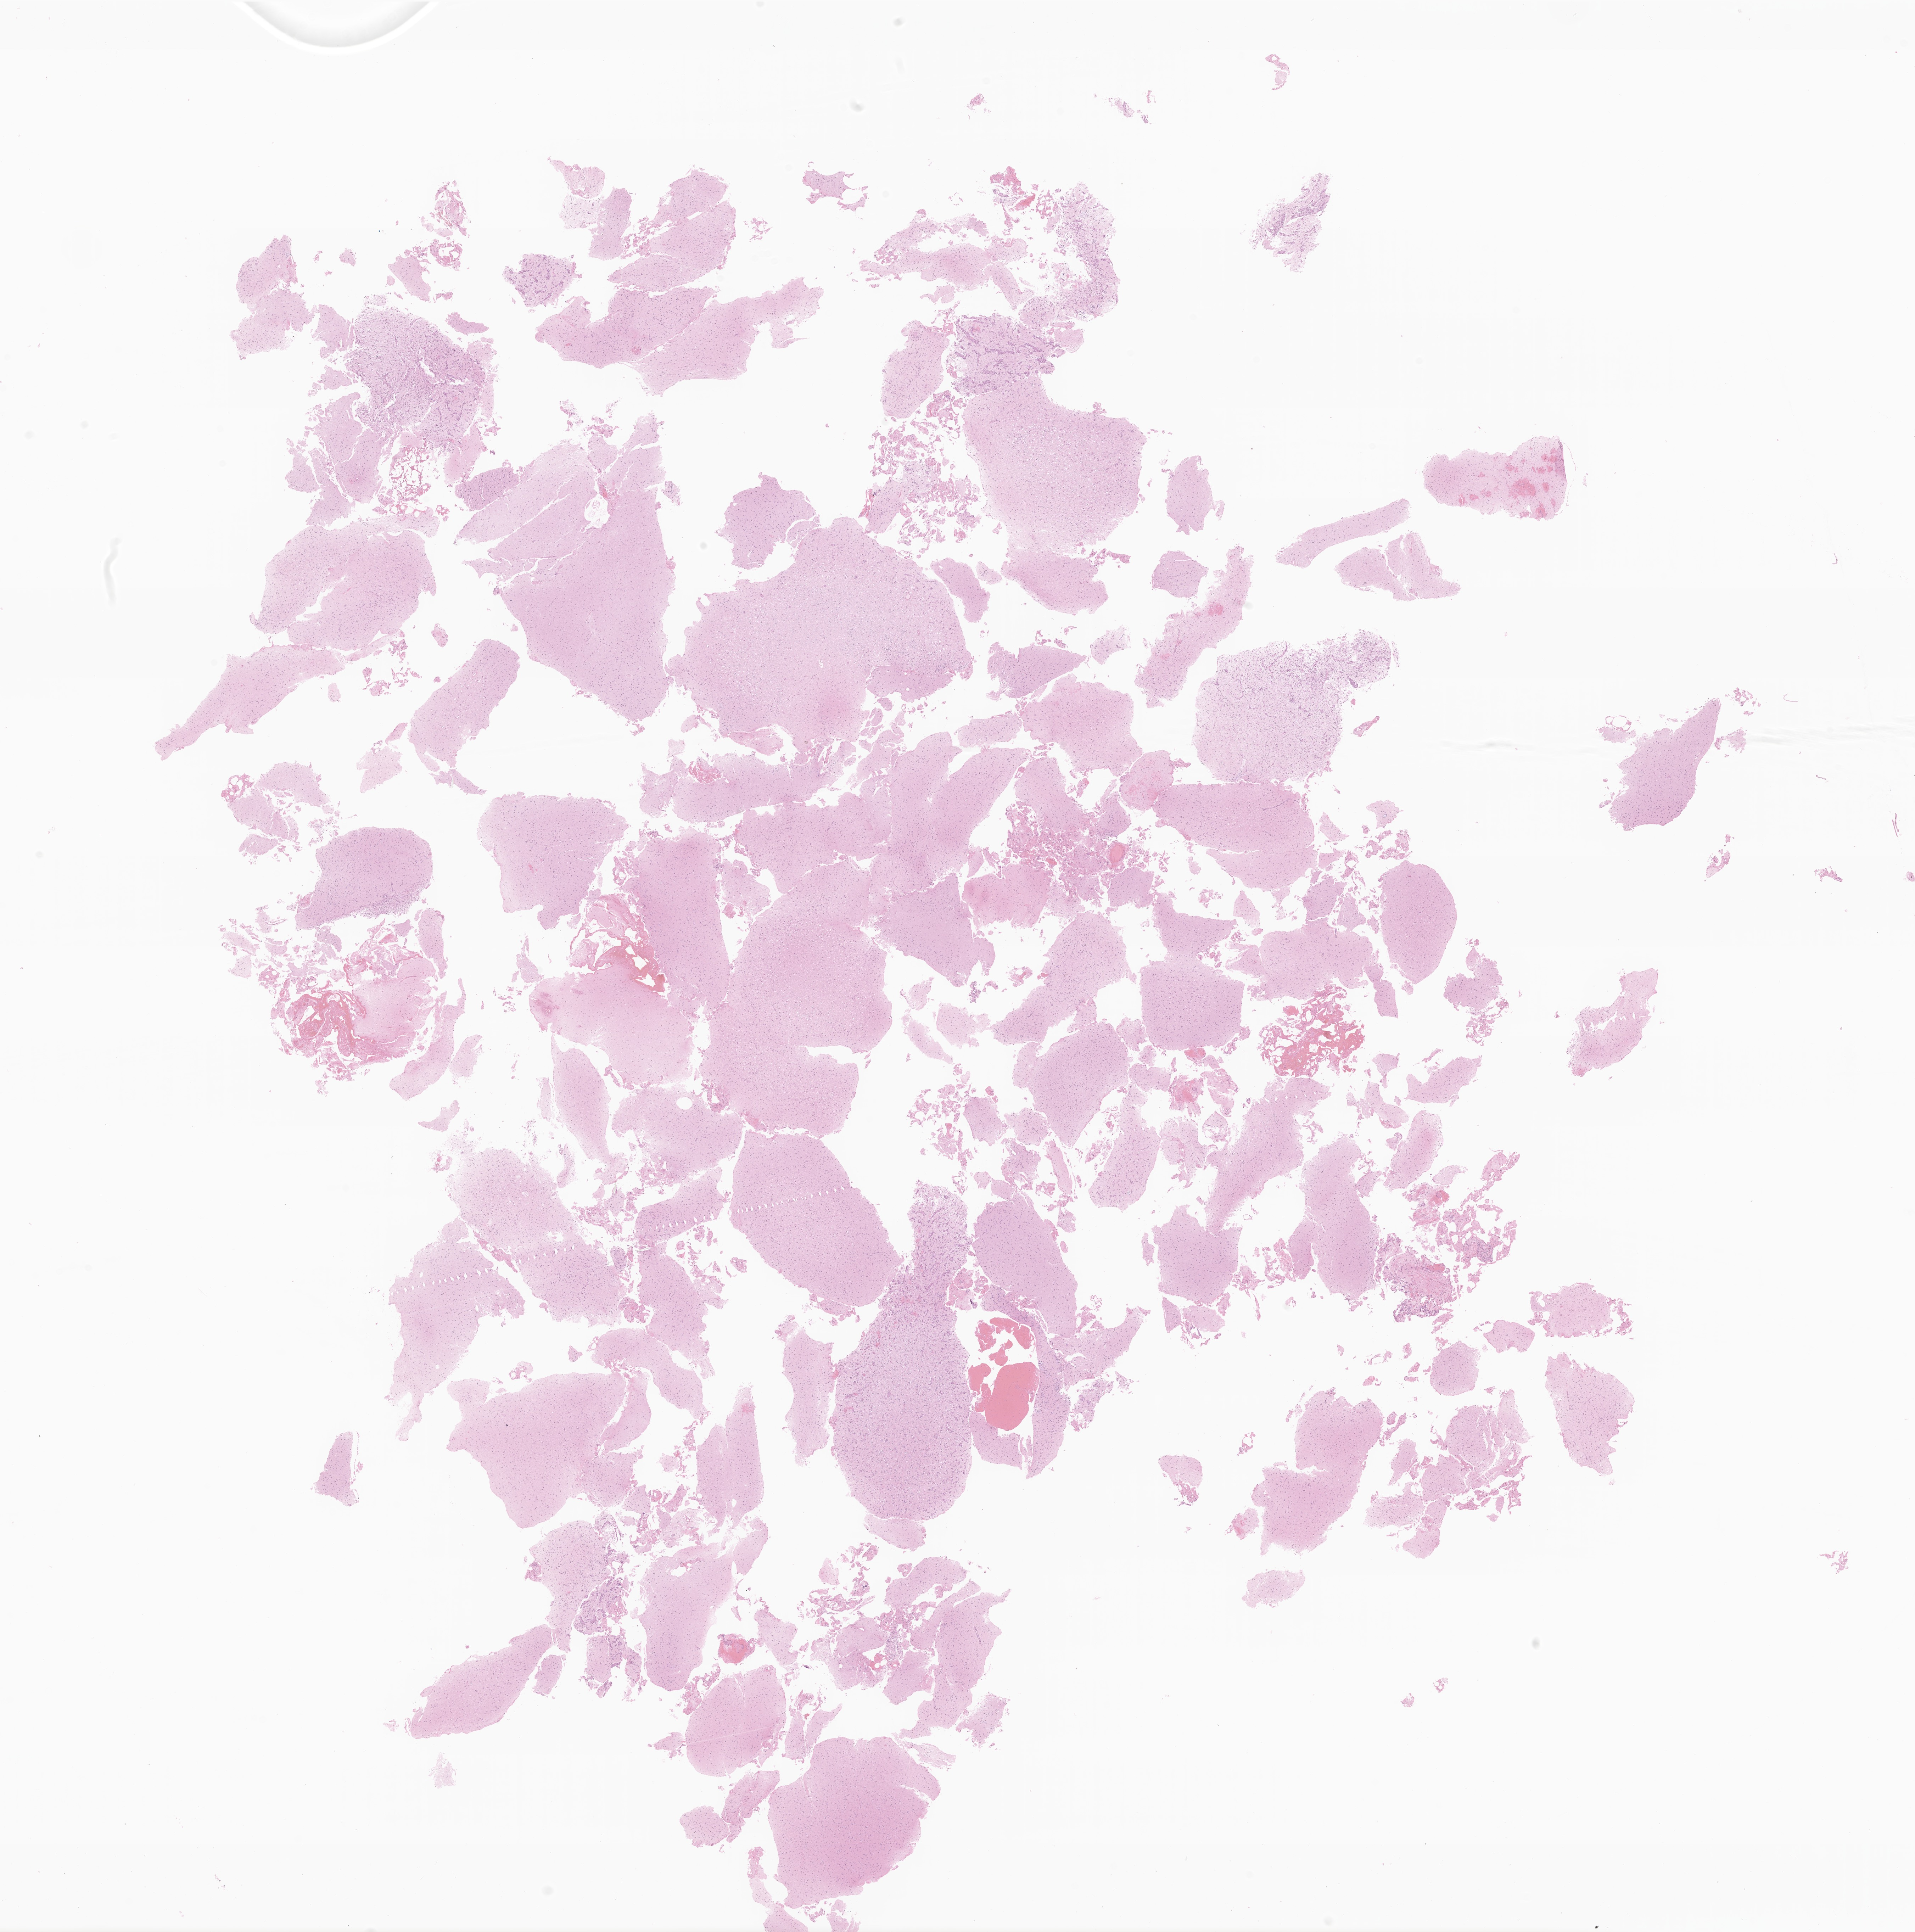
Whole-slide image, haematoxylin and eosin stain of tumor tissue from the temporal lobe — low-resolution overview of the scanned area, about 22.8 x 23.0 mm. FFPE section. Female patient, age 336 days.
Diagnosis (ICD-O-3 morphology term): Neoplasm, malignant.